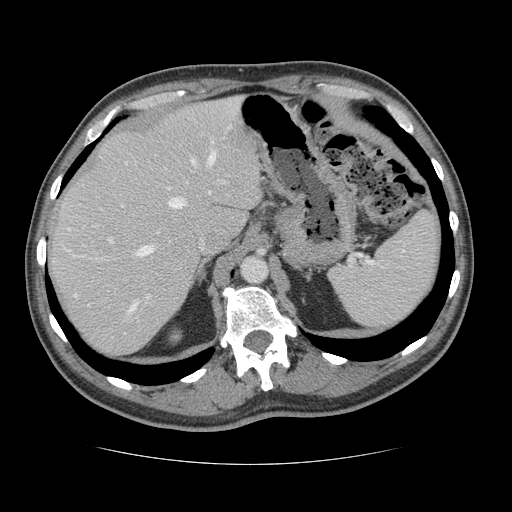
Contrast-enhanced abdominal CT, one axial slice; position 95 of 134 along the scan axis; intravenous contrast given; soft-tissue window (W 400 / L 40 HU); 512 × 512 image matrix. Male patient, age 68 years. Case-level facts recorded for this patient, not image findings: diagnosis: colorectal cancer liver metastases, imaged before liver resection; multiple liver metastases: yes; largest metastasis: 2.2 cm; chemotherapy before resection: no.
Annotated regions visible in this slice (expert manual segmentation):
- hepatic veins: bounding box <74,141,215,313> (left, top, right, bottom; pixels)
- liver: <50,99,262,357>
- planned liver remnant (the part of the liver to remain after resection): <49,99,262,332>
- portal vein (with intrahepatic branches): <109,205,150,297>